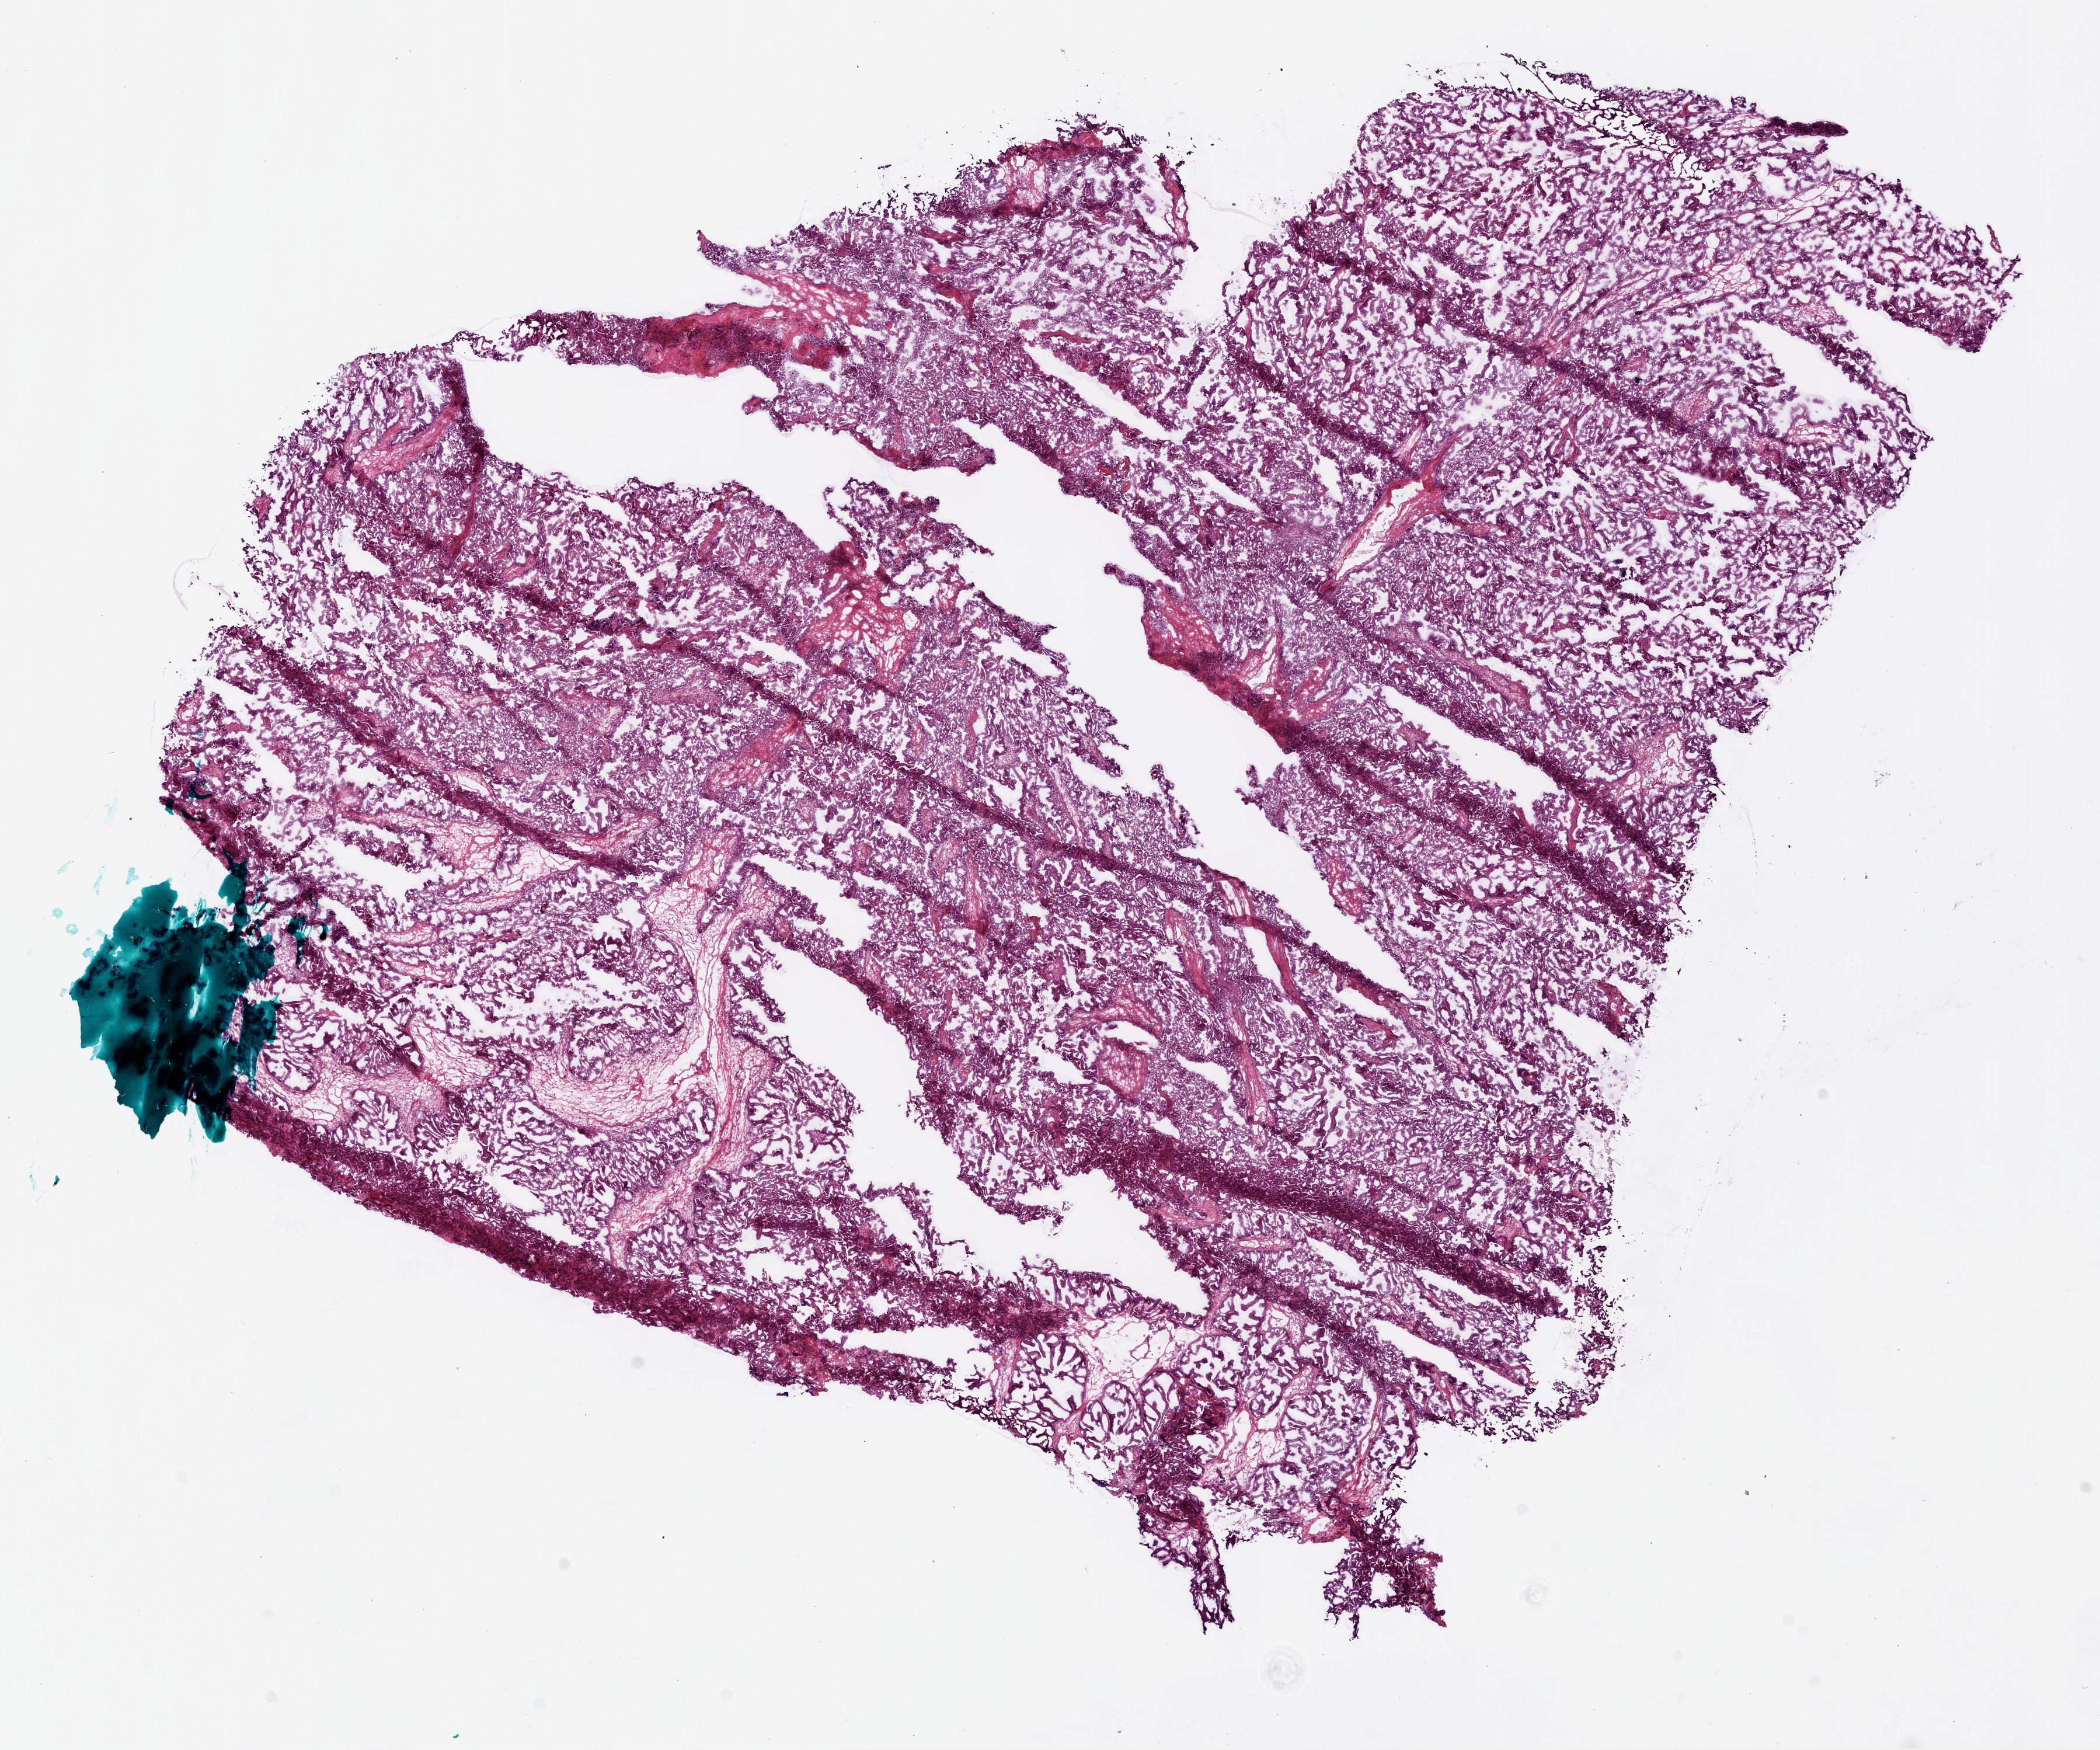
Hematoxylin and eosin (H&E) stained whole-slide image, shown as a low-resolution overview of the whole scanned area (about 14.5 x 12.1 mm); frozen section; sample: primary tumour, ovary. Female patient; age at initial diagnosis 50 years. Histologic grade: G3 (poorly differentiated). Composition of this section per pathologist review: tumour cells 0%, tumour nuclei 90%, normal cells 0%, stromal cells 0%, necrosis 5%.
• pathologic diagnosis: Serous cystadenocarcinoma, NOS
• FIGO stage: IIIC